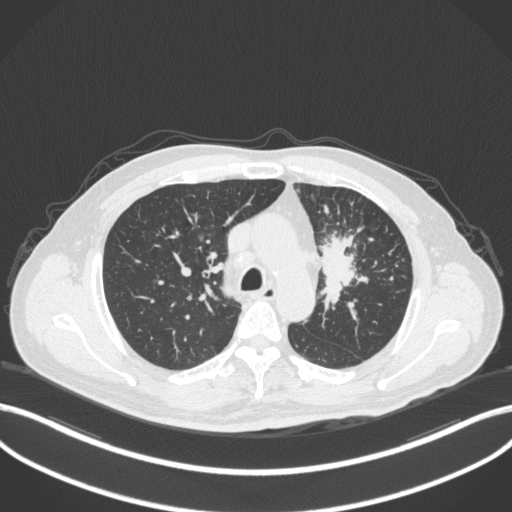
Chest CT, one axial slice. Position 246 of 386 along the scan axis. 120 kVp. Lung window (W 1500 / L -600 HU). 1 mm slice thickness. 512 × 512 image matrix. Patient: male, 69 years. From the clinical record (not read from this slice): clinical TNM (as recorded): T2a N2 M0.
Outlined on this slice (bounding box drawn by a radiologist):
- lung tumour (recorded histology: adenocarcinoma): bounding box <317,230,365,308> (left, top, right, bottom; pixels)